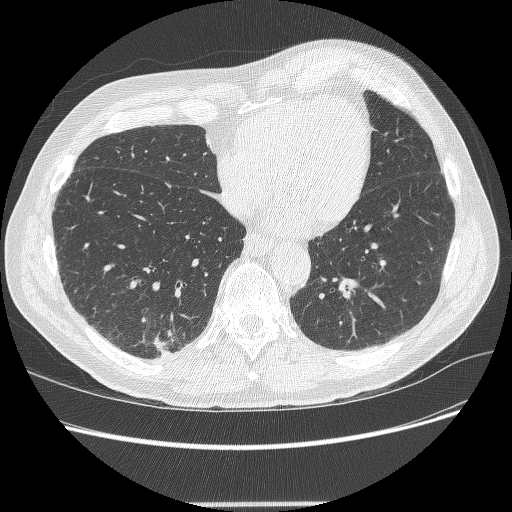
Low-dose screening chest CT, axial slice; second screening round (one year after baseline); lung window (W 1500 / L -600 HU); lung (sharp) reconstruction kernel (BONE); slice 77 of 245 in the series. Male, age 71 years at enrolment.
Expert-annotated lung lesion, bounding box [x1, y1, x2, y2] px = [137, 323, 190, 365]. The screening reader recorded 5 non-calcified nodules or masses ≥4 mm on this exam (right lower lobe, right lower lobe, right upper lobe, right upper lobe, right upper lobe); which of them this box marks is not recorded. Lung cancer was diagnosed 7 days after this screen: squamous cell carcinoma, NOS, right lower lobe, moderately differentiated (G2), stage IA (AJCC 6th edition), 27 mm at pathology.